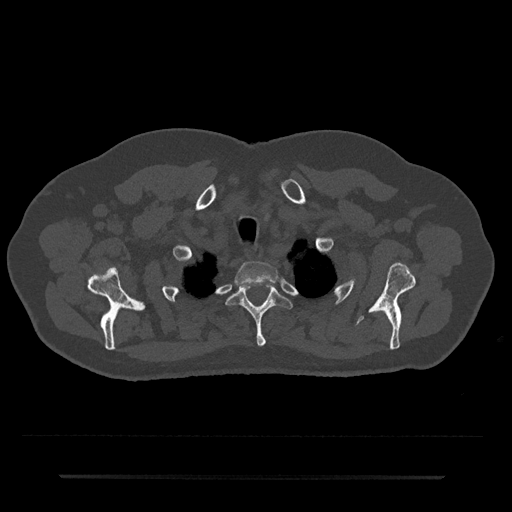
CT including the spine, one axial slice. Slice 613 of 797 in the series (ordered by position). Reconstruction kernel Br40s/3. 120 kVp. Bone window (W 1800 / L 400 HU). 0.5 mm slice thickness. 512 × 512 image matrix, field of view 437 × 437 mm. Patient: male, 69 years. Case-level facts recorded for this patient, not image findings: primary cancer: prostate.
Annotated regions visible in this slice (semi-automatically segmented with operator editing):
- T1 vertebra: bounding box <235,261,279,287> (left, top, right, bottom; pixels)
- T2 vertebra: <226,281,293,347>